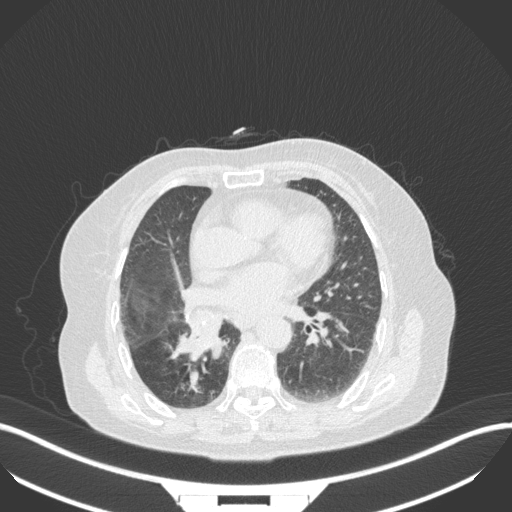
Chest CT, one axial slice. Slice 146 of 329 in the series (ordered by position). Reconstruction kernel B31f. 120 kVp. Lung window (W 1500 / L -600 HU). 1 mm slice thickness. 512 × 512 image matrix, field of view 400 × 400 mm. Patient: female, 75 years. From the clinical record (not read from this slice): clinical TNM (as recorded): T1b N0 M1a; histopathological grade: G1.
Structures marked on this image (bounding box drawn by a radiologist):
- lung tumour (recorded histology: squamous cell carcinoma): box from (x=170, y=314) to (x=224, y=363) px